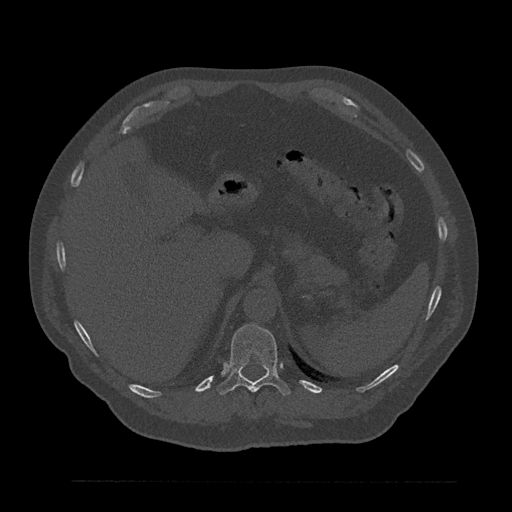
CT including the spine, one axial slice; slice 298 of 797 in the series (ordered by position); reconstruction kernel Br40s/3; 120 kVp; bone window (W 1800 / L 400 HU); 512 × 512 image matrix. Patient: male, 61 years. Case-level facts recorded for this patient, not image findings: primary cancer: prostate.
Outlined on this slice (semi-automatic segmentation, software-assisted and operator-edited):
- T11 vertebra: bounding box (x1, y1, x2, y2) in pixels: (217, 324, 290, 396)